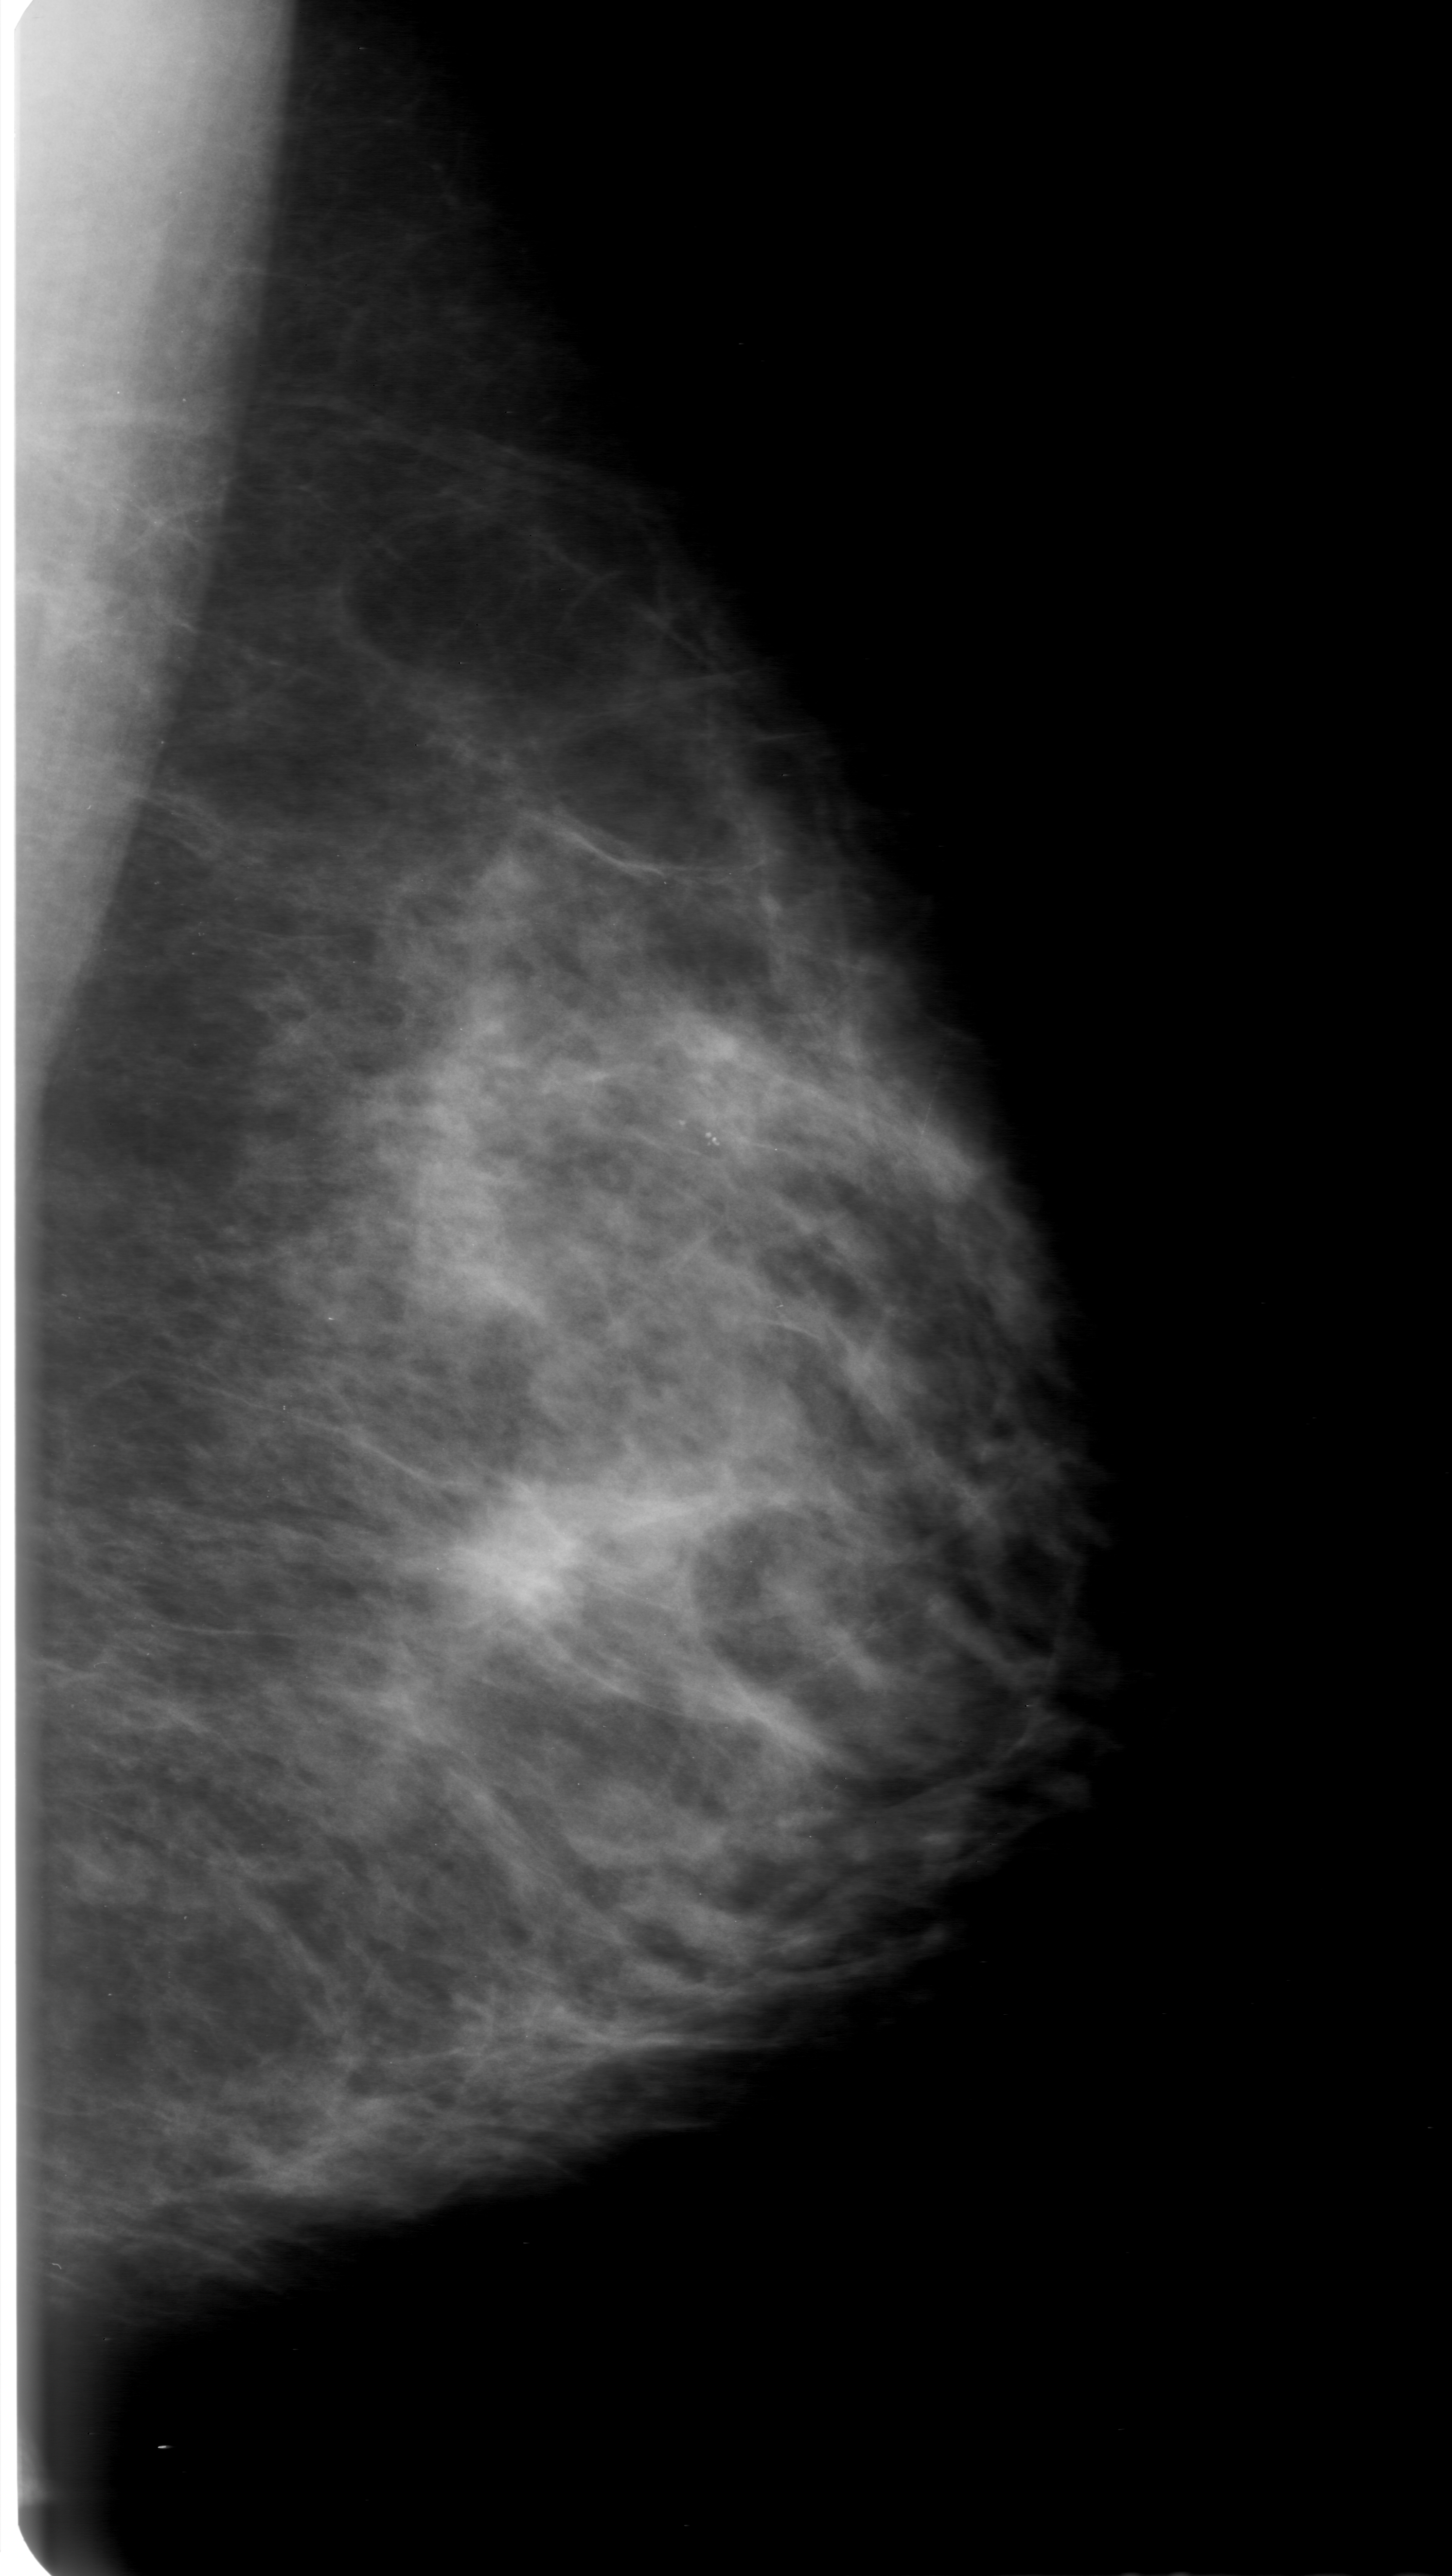
Digitized screen-film mammogram, left breast, mediolateral oblique (MLO) view.
- Radiologist-marked abnormalities on this image: mass, shape oval, margins microlobulated; BI-RADS assessment category 0 (incomplete: needs additional imaging); subtlety rating 4 on a 1 (subtle) to 5 (obvious) scale; pathology (as recorded): malignant.